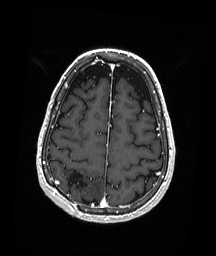
Brain MRI from a brain-tumour surgery series, one axial slice; slice 61 of 192 in the series (ordered by position); T1-weighted post-contrast; 216 × 256 image matrix. Case-level facts recorded for this patient, not image findings: histopathology: Astrocytoma; WHO grade: 3; IDH mutation: yes; tumour location: Right Parietal.
Outlined on this slice (expert manual segmentation):
- previous resection cavity: bounding box <67,170,87,195> (left, top, right, bottom; pixels)